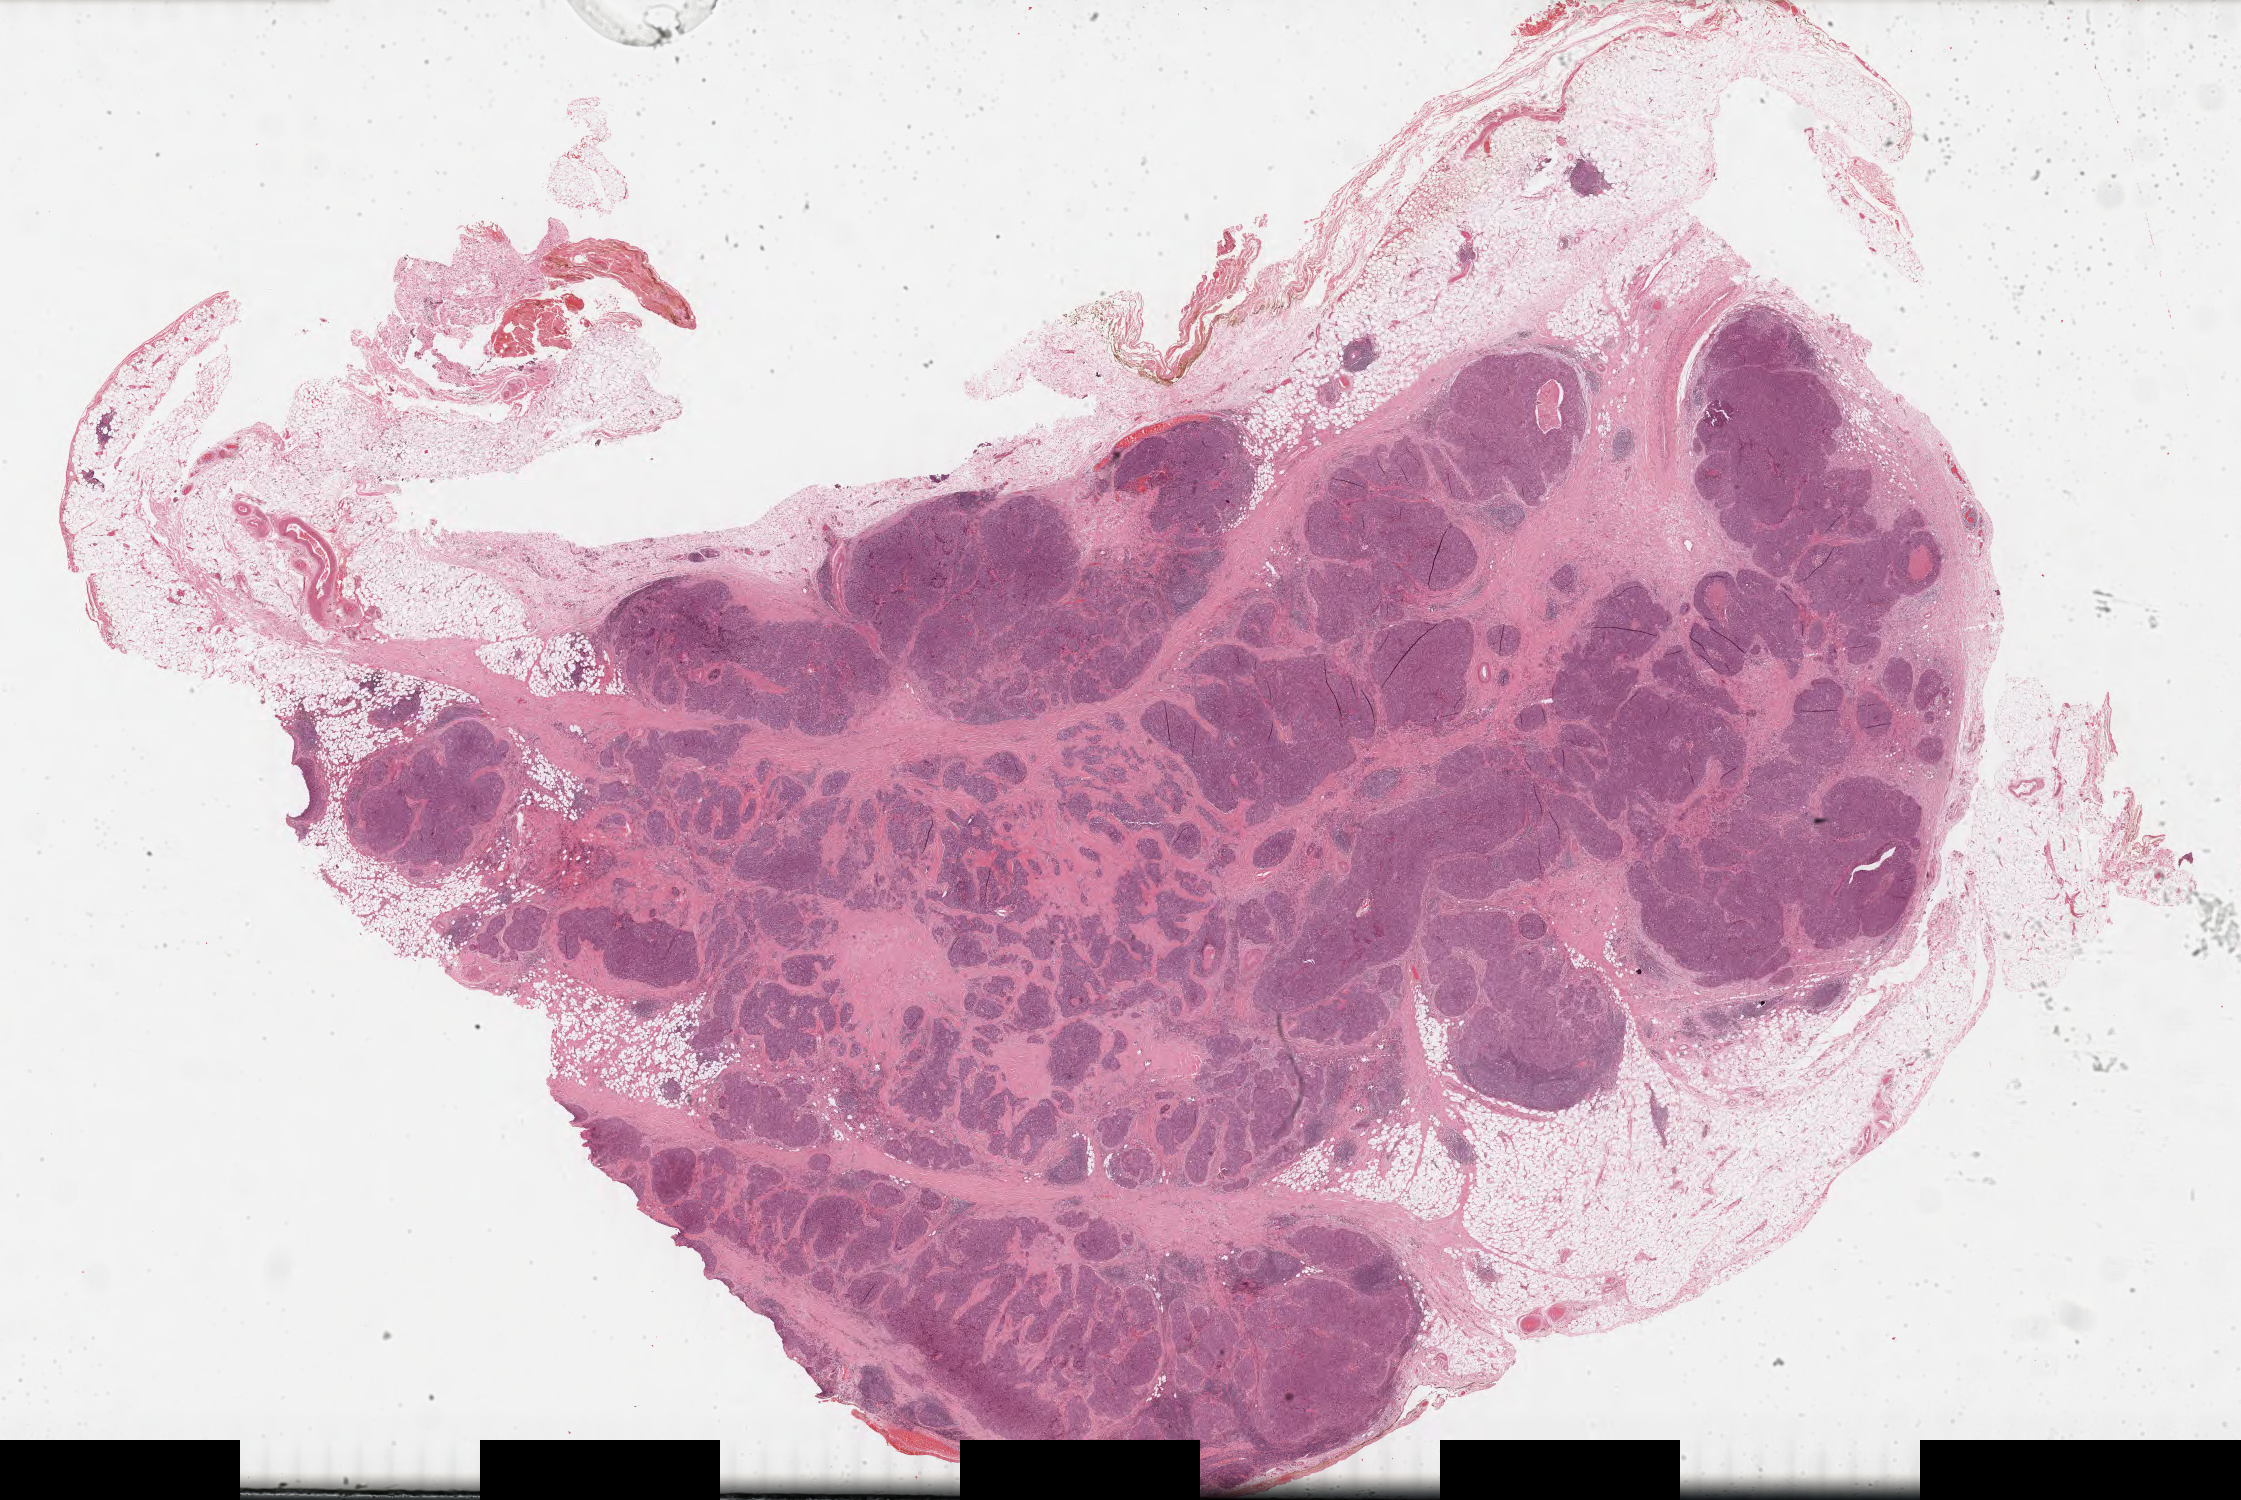
Whole-slide histology image, Hematoxylin and eosin (H&E) stained — whole scanned area (about 35.4 x 23.7 mm, acquisition: 40x scan) shown as a low-resolution overview; FFPE section; sample: primary tumour, thymus. Patient: female, age at initial diagnosis 52 years.
Histologic diagnosis: Thymic carcinoma, NOS.